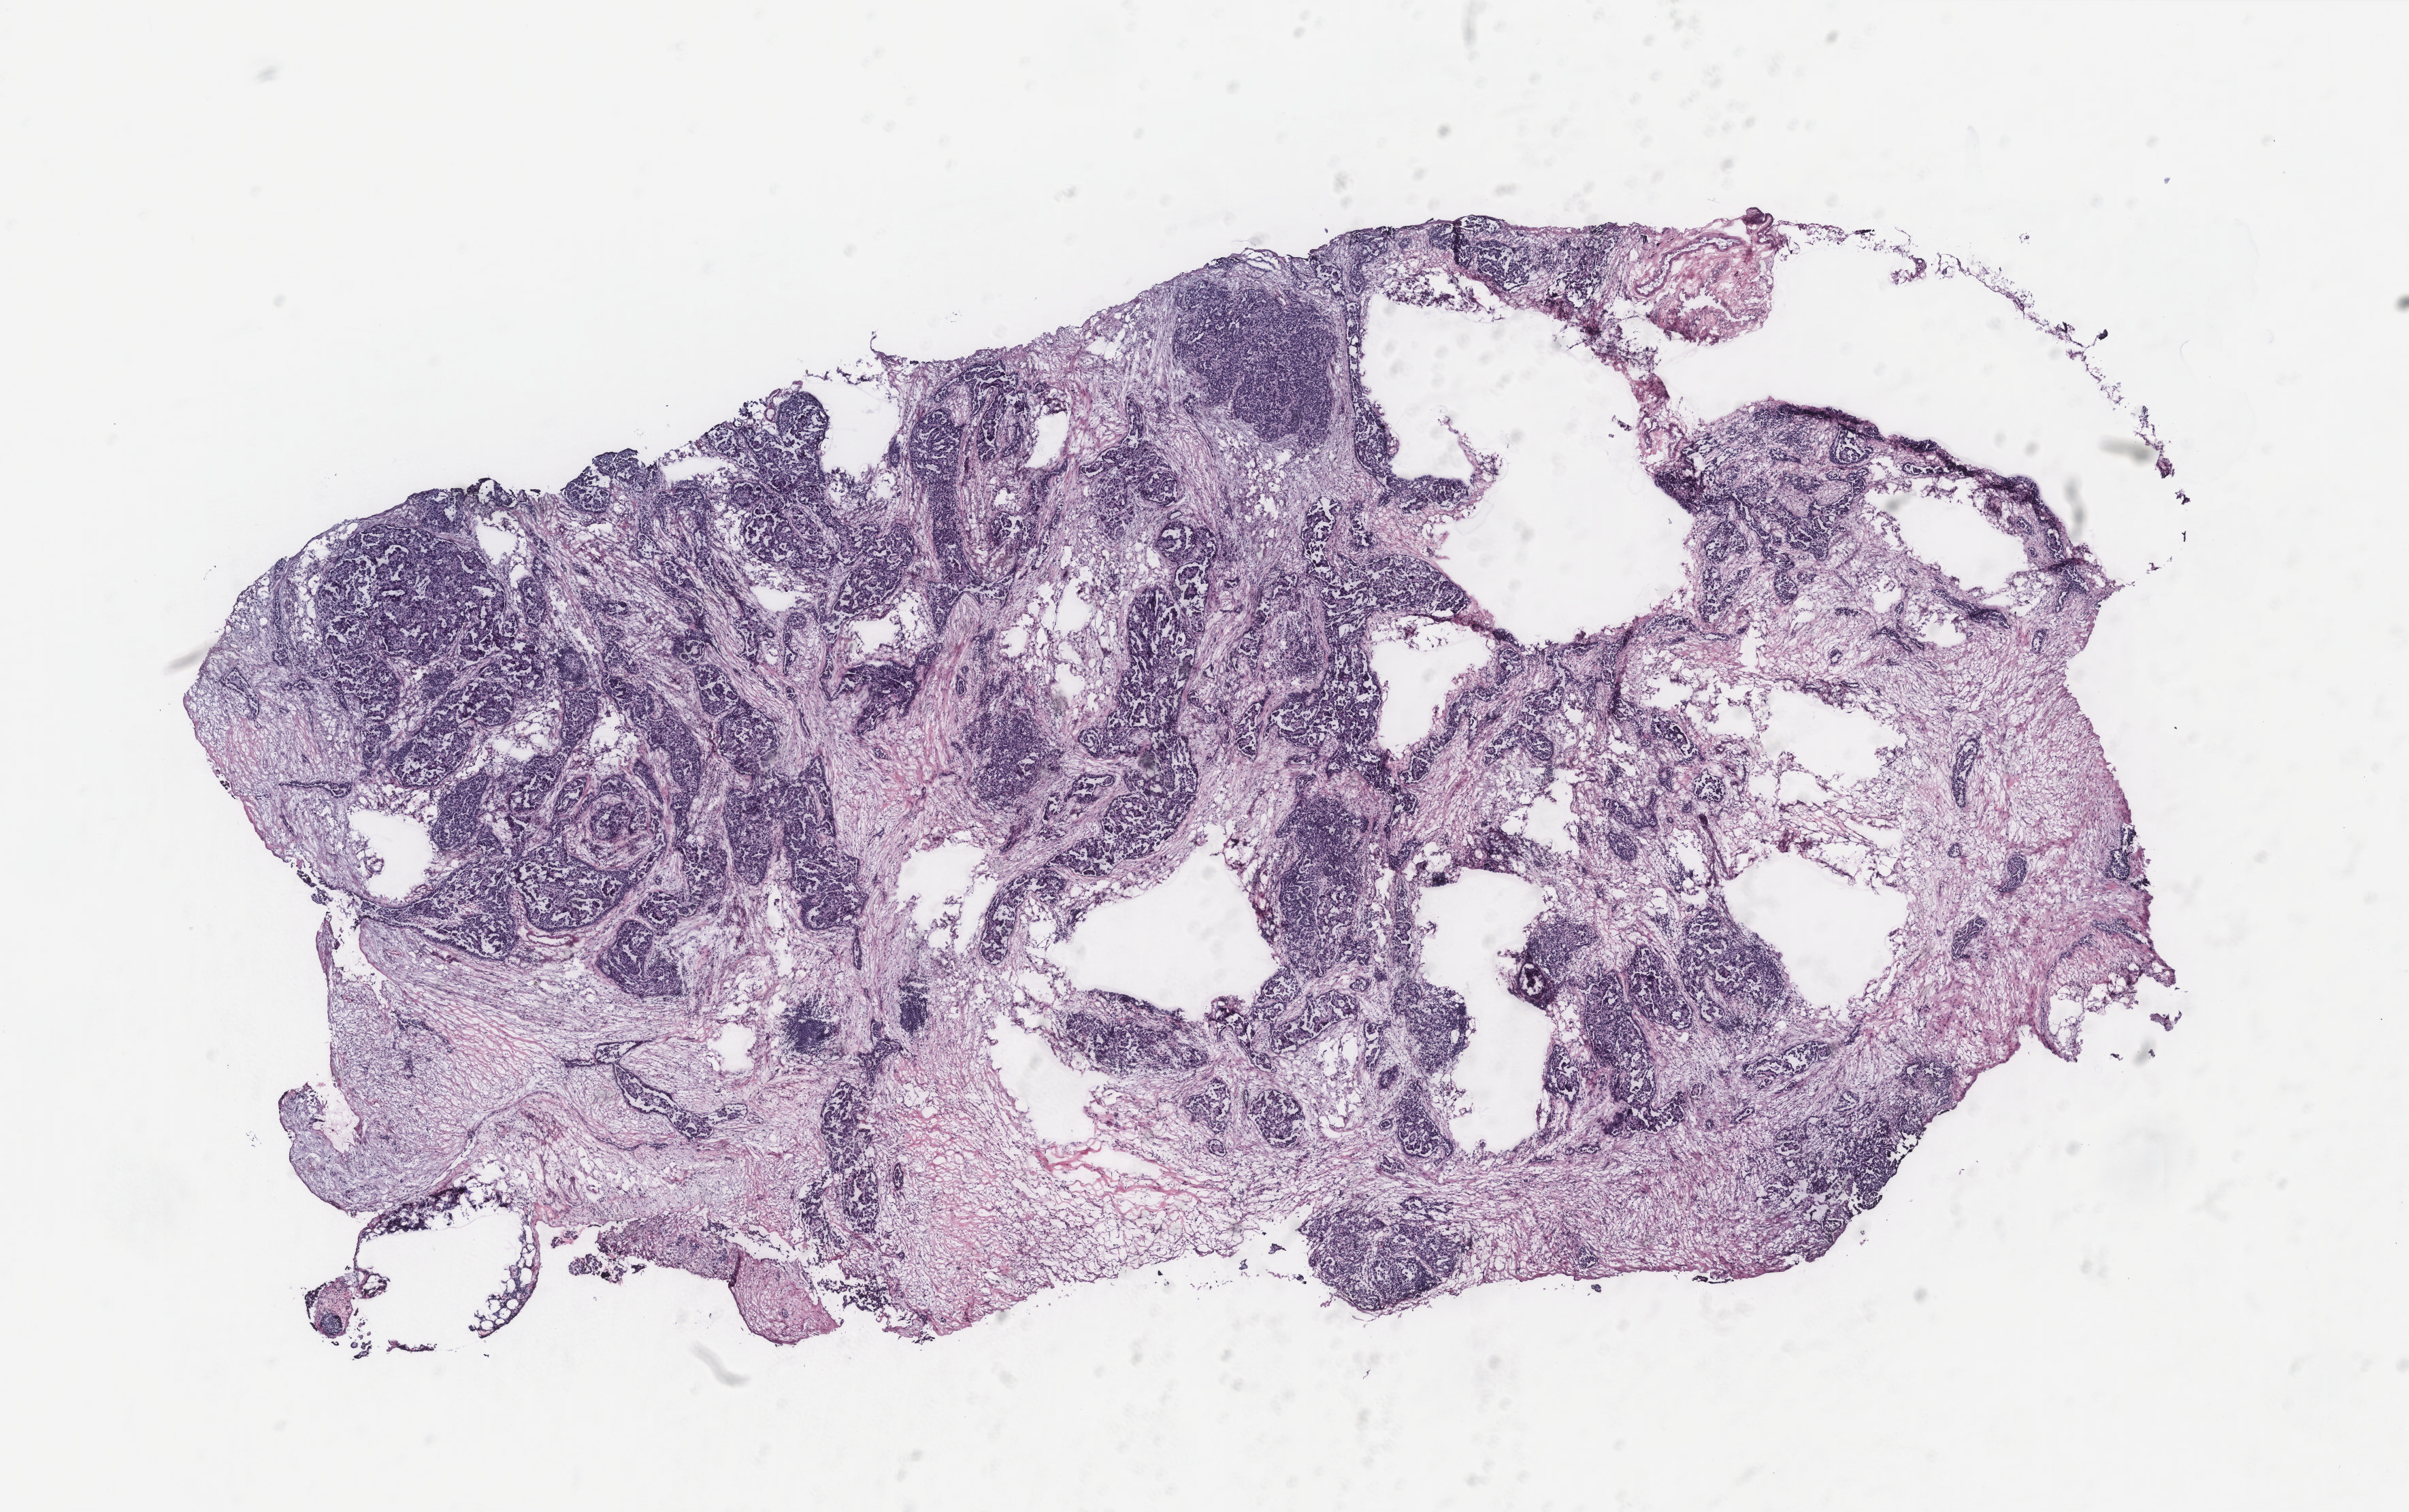
Whole-slide histology image, H&E, a low-resolution overview of the entire scanned area, about 14.2 x 8.9 mm (slide scanned at 40x), tumour tissue sample, ovary. Patient: female, age 77 years.
Diagnosis: Serous adenocarcinoma, NOS (peritoneum, NOS).